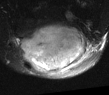
MRI of an extremity soft-tissue mass, one axial slice. Position 21 of 52 along the scan axis. T2-weighted fat-saturated. MR volume resampled by the dataset authors to the PET/CT grid (not the native acquisition matrix). 109 × 95 image matrix. Male patient. Case-level facts recorded for this patient, not image findings: histological type: synovial sarcoma; site of the primary tumour: left poplietal fossa.
Structures marked on this image (expert contour drawn on MRI and transferred to this co-registered scan by the dataset authors):
- gross tumour volume (mass): bounding box <17,24,89,75> (left, top, right, bottom; pixels)